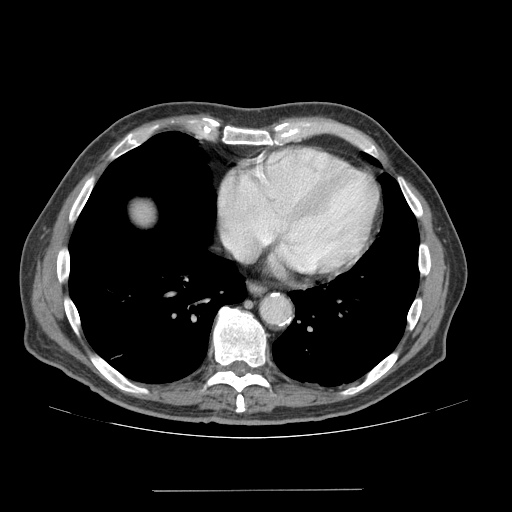
Contrast-enhanced abdominal CT (liver protocol), one axial slice. Position 71 of 77 along the scan axis. Reconstruction kernel STANDARD. 140 kVp. Soft-tissue window (W 400 / L 40 HU). 2.5 mm slice thickness. 512 × 512 image matrix. Case-level facts recorded for this patient, not image findings: diagnosis: hepatocellular carcinoma (patient treated with transarterial chemoembolisation; whether this scan precedes or follows treatment is not stated here); TNM stage (as recorded): Stage-IVA; Child-Pugh class: A; tumour differentiation: well differentiated; tumour nodularity: uninodular.
Structures marked on this image (semi-automatically segmented with operator editing):
- liver parenchyma outside the tumour (the mass and vessels are separate outlines, so this box may not span the whole liver): bounding box (x1, y1, x2, y2) in pixels: (132, 200, 154, 224)